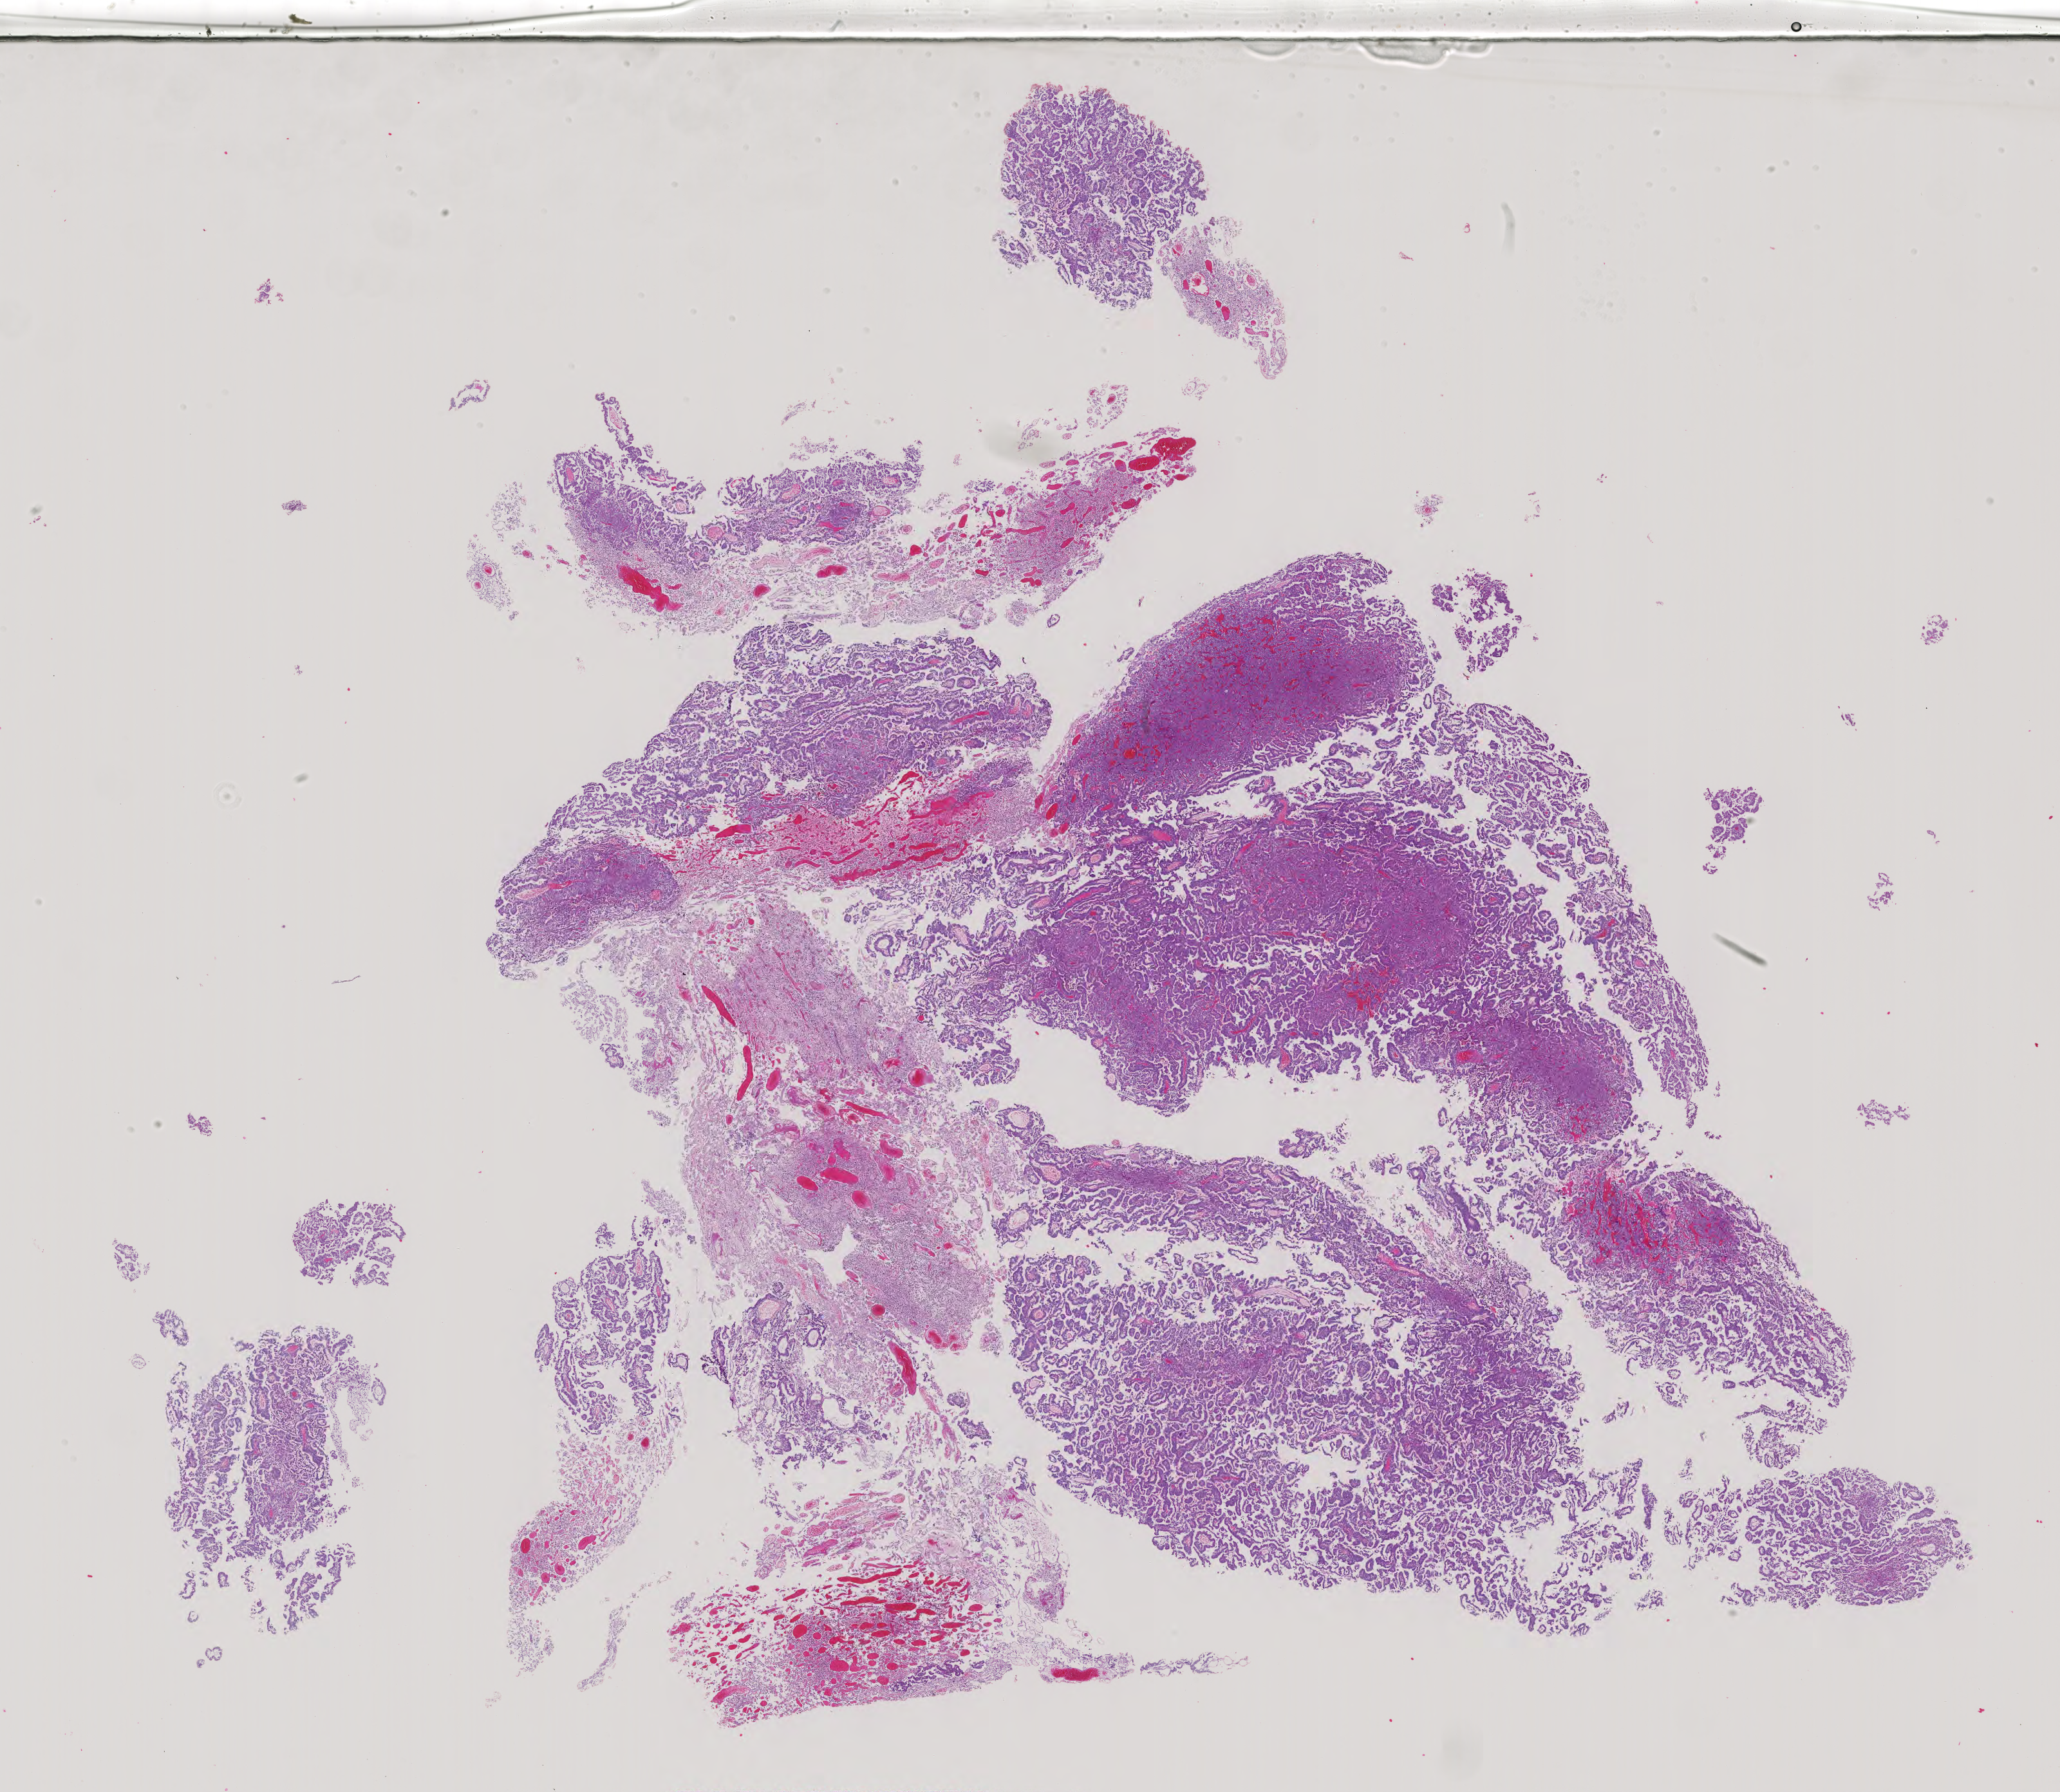
Whole-slide histology image, H&E, shown as a low-resolution overview of the whole scanned area (about 23.3 x 20.3 mm, acquisition: 40x scan); formalin-fixed paraffin-embedded (FFPE) diagnostic section; sample: primary tumour, testis. Male, age 38 years at initial diagnosis.
AJCC pathologic stage: IS (5th edition). Laterality: right. Pathologic diagnosis: Yolk sac tumor.